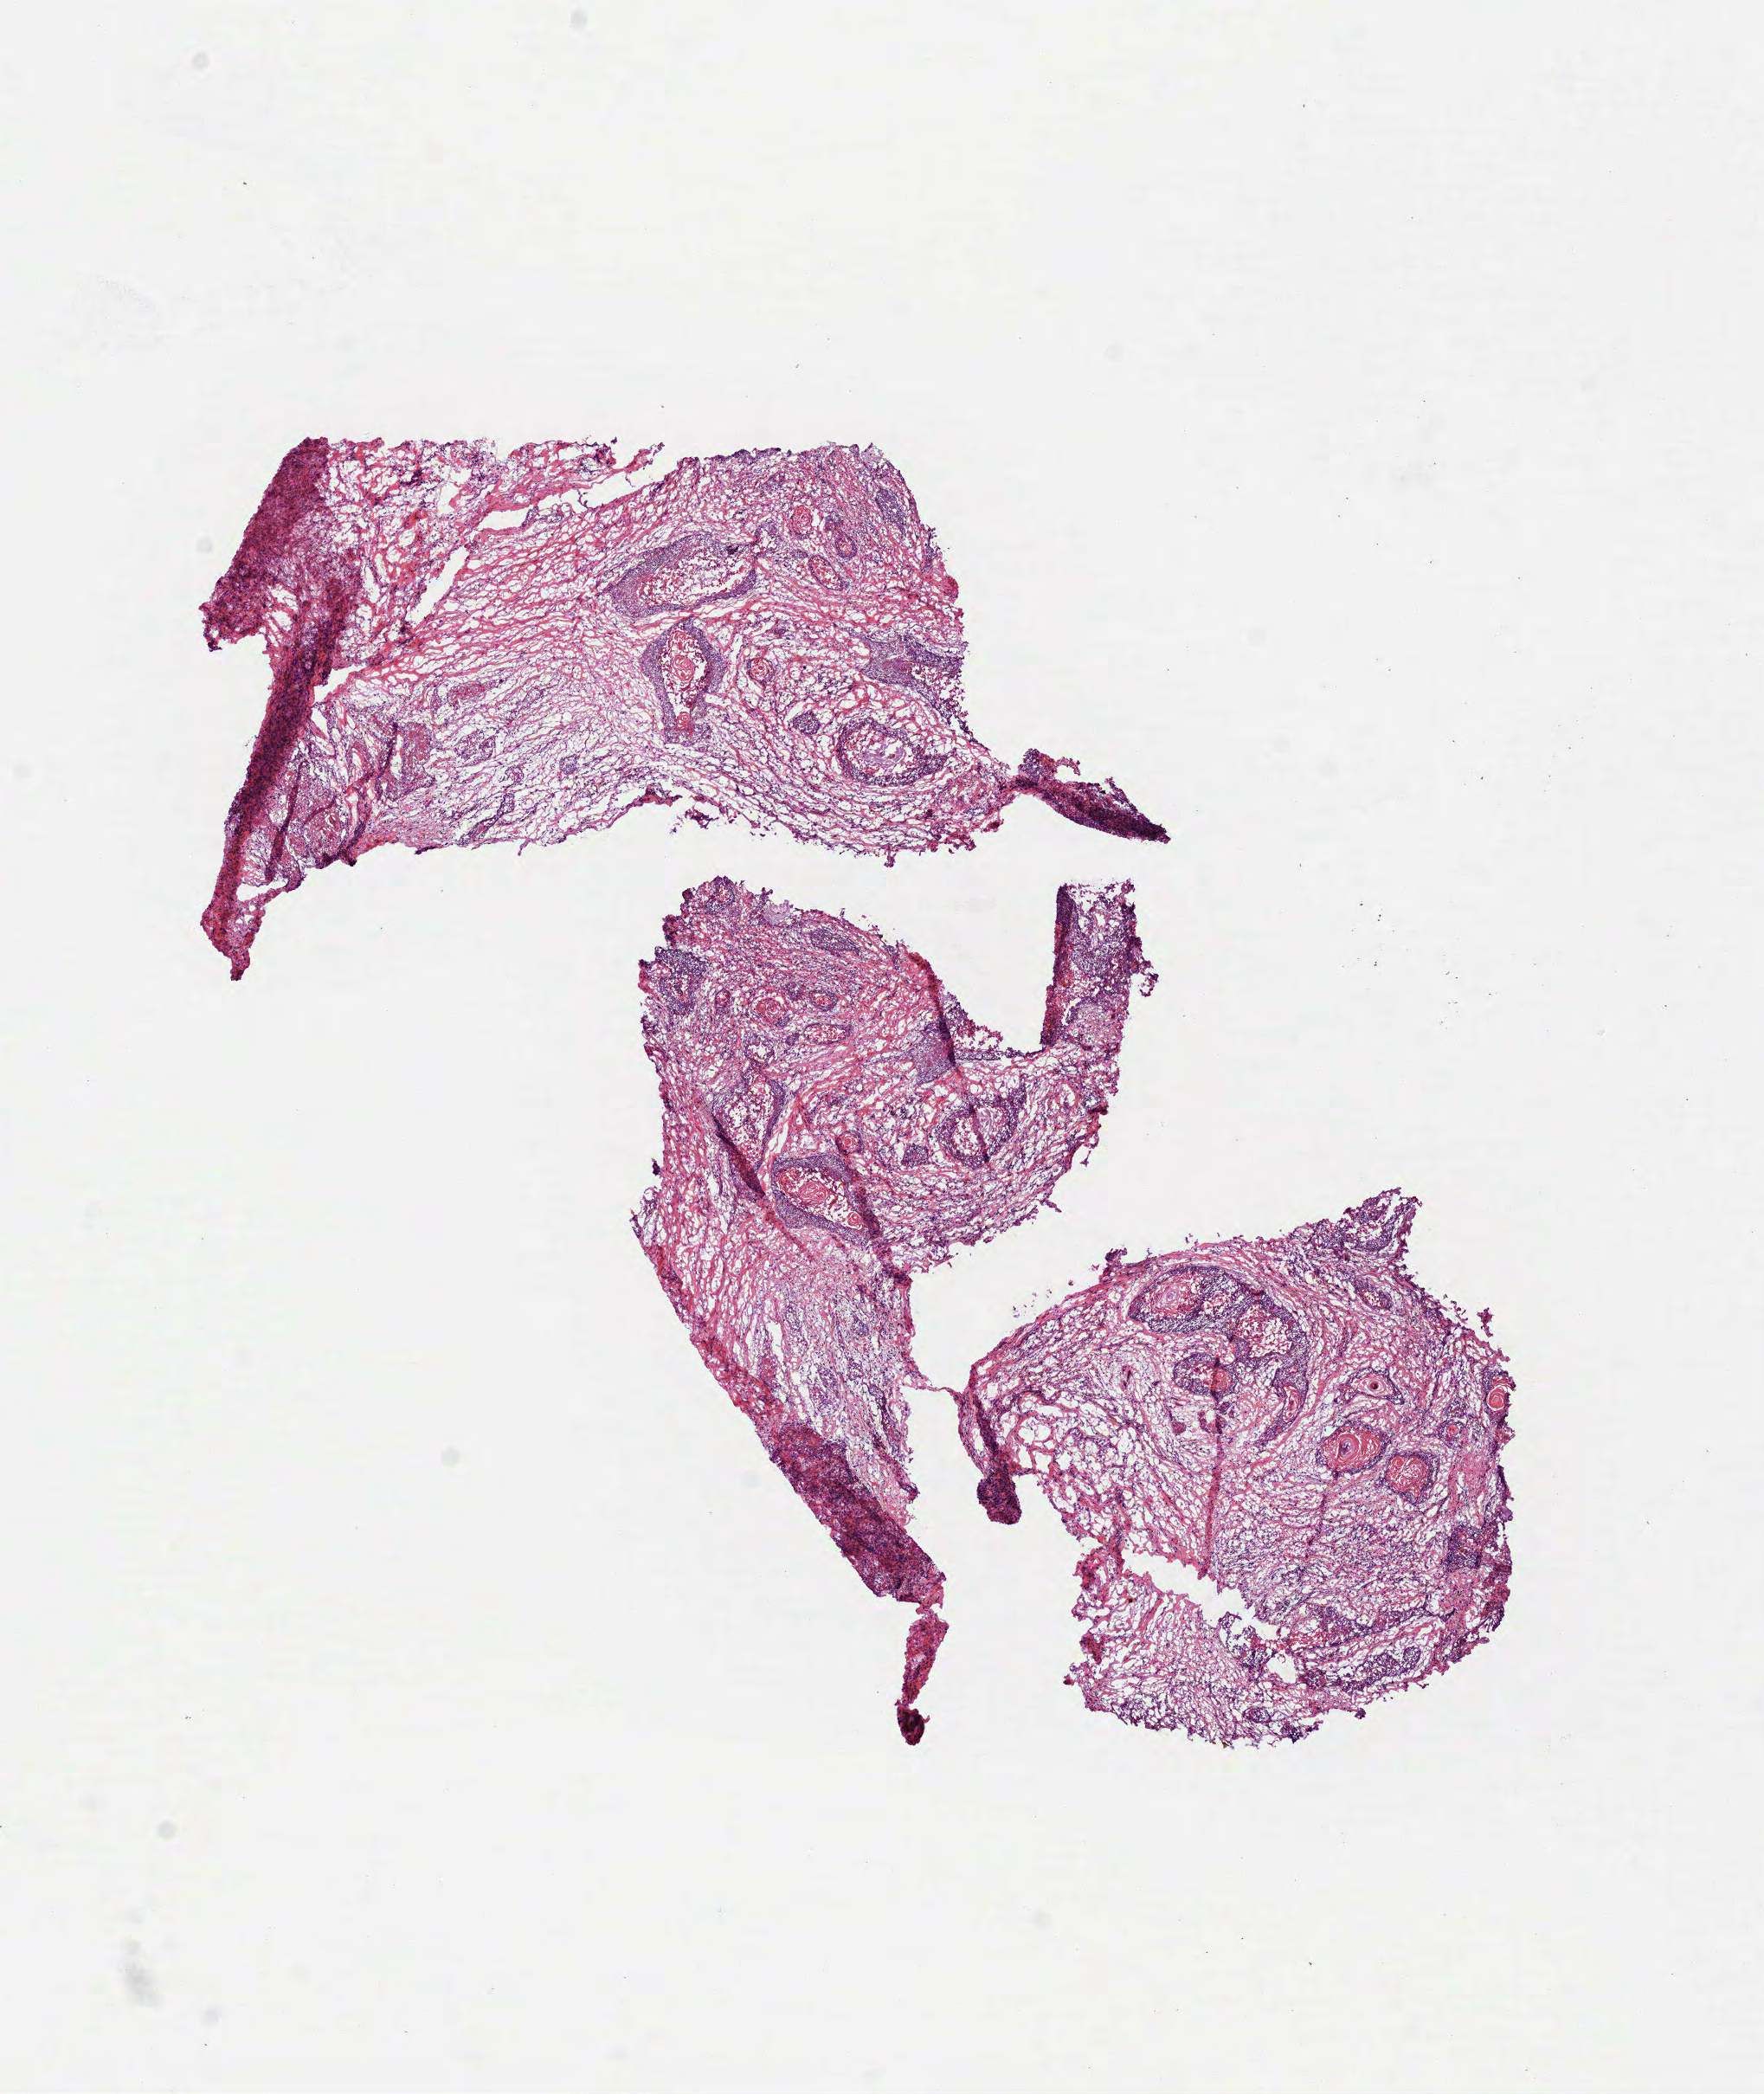
Hematoxylin and eosin (H&E) stained whole-slide image — shown as a low-resolution overview of the whole scanned area (about 8.2 x 9.8 mm, acquisition: 40x scan). Frozen section from the top of the tissue portion. Sample: primary tumour, head and neck. Female patient; age at initial diagnosis 66 years. Histologic grade: G2 (moderately differentiated). Composition of this section per pathologist review: tumour cells 70%, tumour nuclei 60%, normal cells 0%, stromal cells 20%, necrosis 10%. Infiltration values recorded for this section: lymphocyte infiltration 10%, monocyte infiltration 0%, neutrophil infiltration 2%.
Histologic diagnosis: Squamous cell carcinoma, NOS (tongue, NOS). TNM: T3 N2b. AJCC pathologic stage: IVA (7th edition).